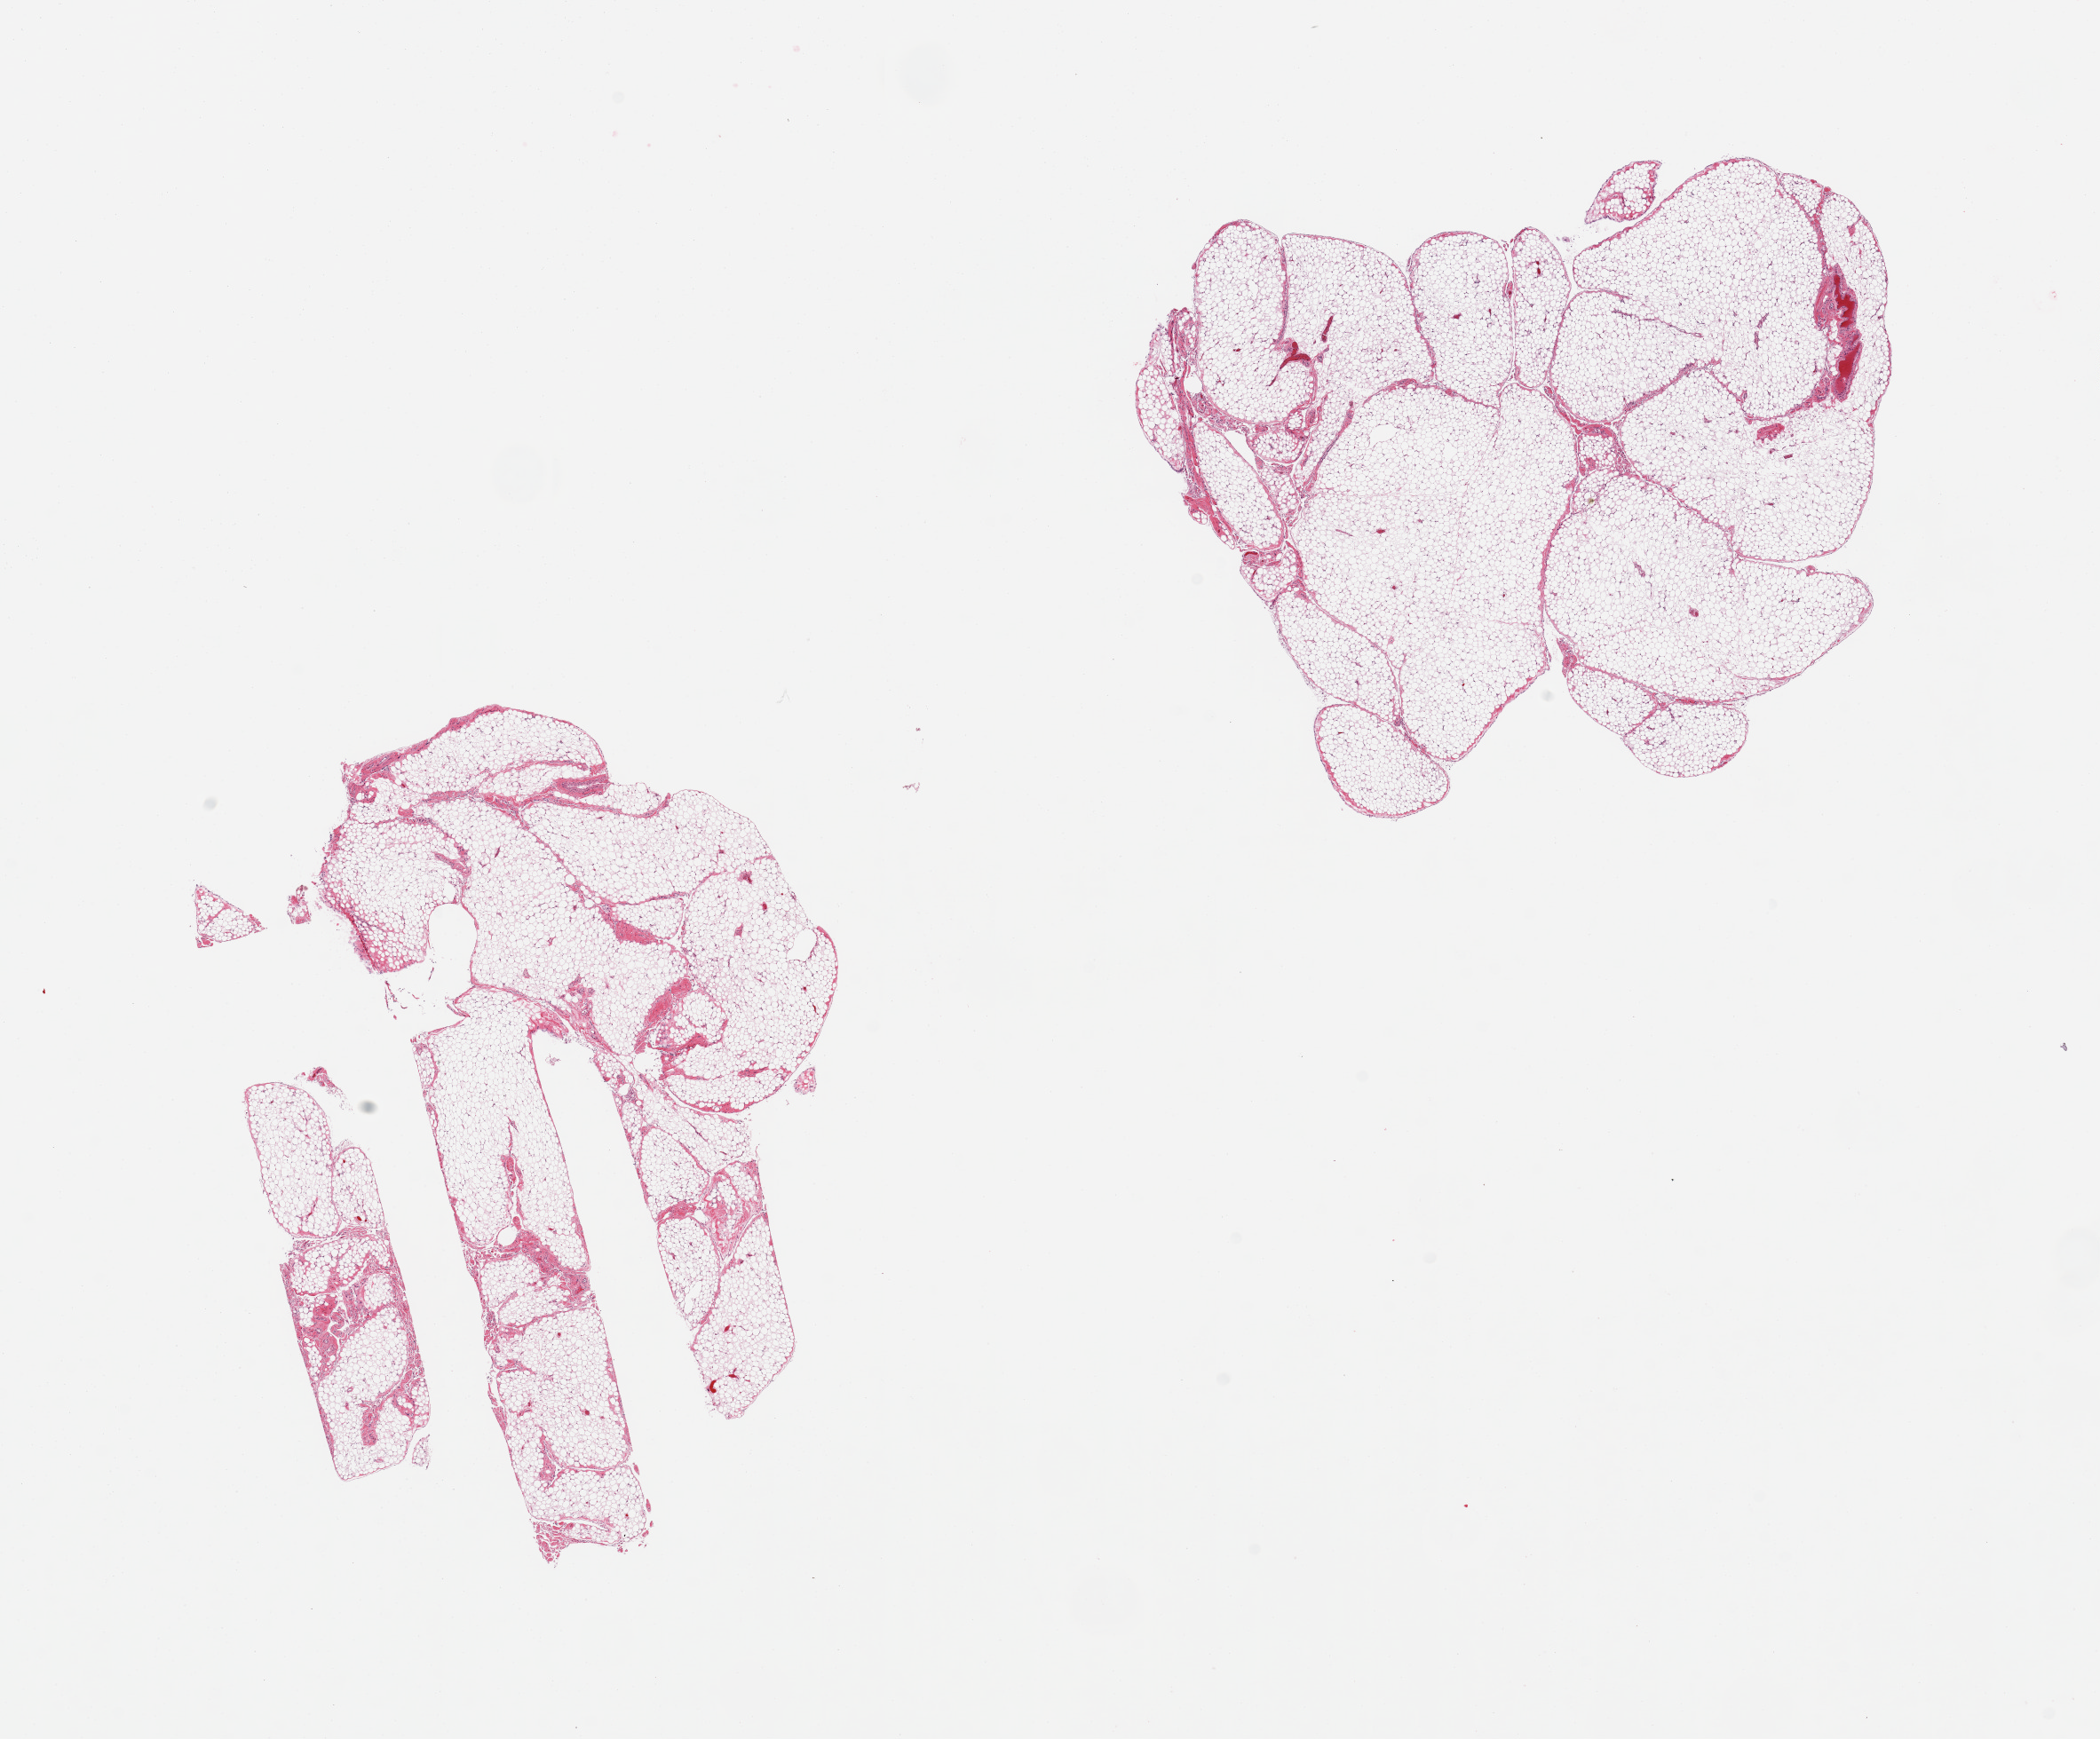
Digitized hematoxylin and eosin (H&E)-stained section, brightfield, a low-resolution overview of the entire scanned area, about 18.7 x 15.5 mm (slide scanned at 20x). PAXgene-fixed paraffin-embedded (PFPE) section. Target tissue: omentum. Donor tissue sample. Donor: female.
Pathologist's review note for this sample: 2 pieces, 10% interstitial fibrous tissue.